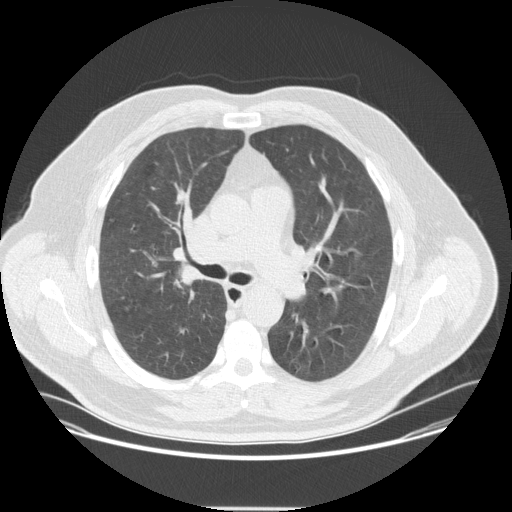
Chest CT (low-dose screening protocol), one axial image; second screening round (one year after baseline); lung window (W 1500 / L -600 HU); 2.5 mm slice thickness; standard (soft-tissue) reconstruction kernel (STANDARD); slice 130 of 351 in the series. Male participant, aged 57 years at enrolment. Current smoker at enrolment.
• Lesion marked by an expert reader, bounding box <157,256,211,304> (left, top, right, bottom; pixels).
• The exam's reader record, not a measurement of the box and not confirmed to be the same lesion: non-calcified nodule or mass ≥4 mm, right upper lobe, 20 × 16 mm, spiculated (stellate) margins, soft tissue attenuation, pre-existing on the prior screen: no.
• Official screen result: positive, other.
• Later outcome: lung cancer diagnosed 35 days after this screen — non-small cell carcinoma, right upper lobe, poorly differentiated (G3), stage IIA (AJCC 6th edition), 25 mm at pathology.